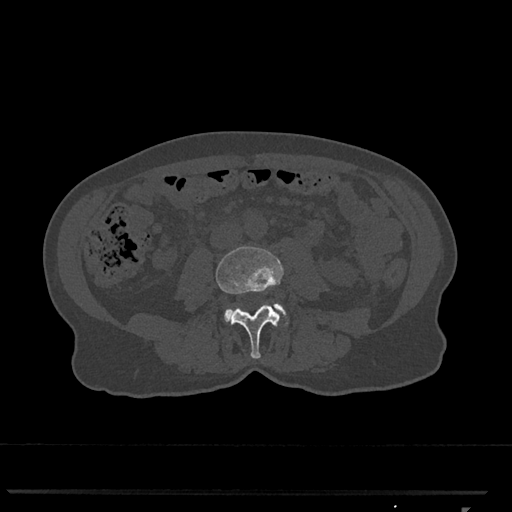
CT including the spine, one axial slice. Position 254 of 793 along the scan axis. Reconstruction kernel Br40s/3. 120 kVp. Bone window (W 1800 / L 400 HU). 0.5 mm slice thickness. 512 × 512 image matrix, field of view 380 × 380 mm. Female patient, age 62 years. Case-level facts recorded for this patient, not image findings: primary cancer: renal.
Structures marked on this image (semi-automatically segmented with operator editing):
- L3 vertebra: bounding box (x1, y1, x2, y2) in pixels: (216, 246, 283, 359)
- L4 vertebra: (224, 303, 286, 322)